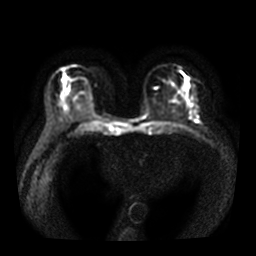
Breast MRI, one axial slice; slice 18 of 36 in the series (ordered by position); diffusion-weighted series; image 2 of 4 stored at this slice position (different b-values; order by instance number); 3 T; 5 mm slice thickness; 256 × 256 image matrix, field of view 320 × 320 mm. Female patient.
Annotated regions visible in this slice (expert manual segmentation):
- tumour on diffusion-weighted imaging: box from (x=185, y=78) to (x=192, y=107) px